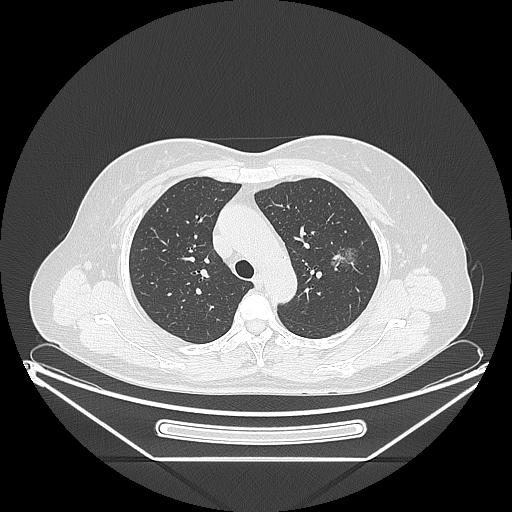
Chest CT, one axial slice. Position 156 of 226 along the scan axis. 120 kVp. Lung window (W 1500 / L -600 HU). 1.25 mm slice thickness. 512 × 512 image matrix. Patient: female, 54 years. From the clinical record (not read from this slice): clinical TNM (as recorded): T1c N0 M0.
Structures marked on this image (bounding box drawn by a radiologist):
- lung tumour (recorded histology: adenocarcinoma): bounding box <320,238,366,281> (left, top, right, bottom; pixels)